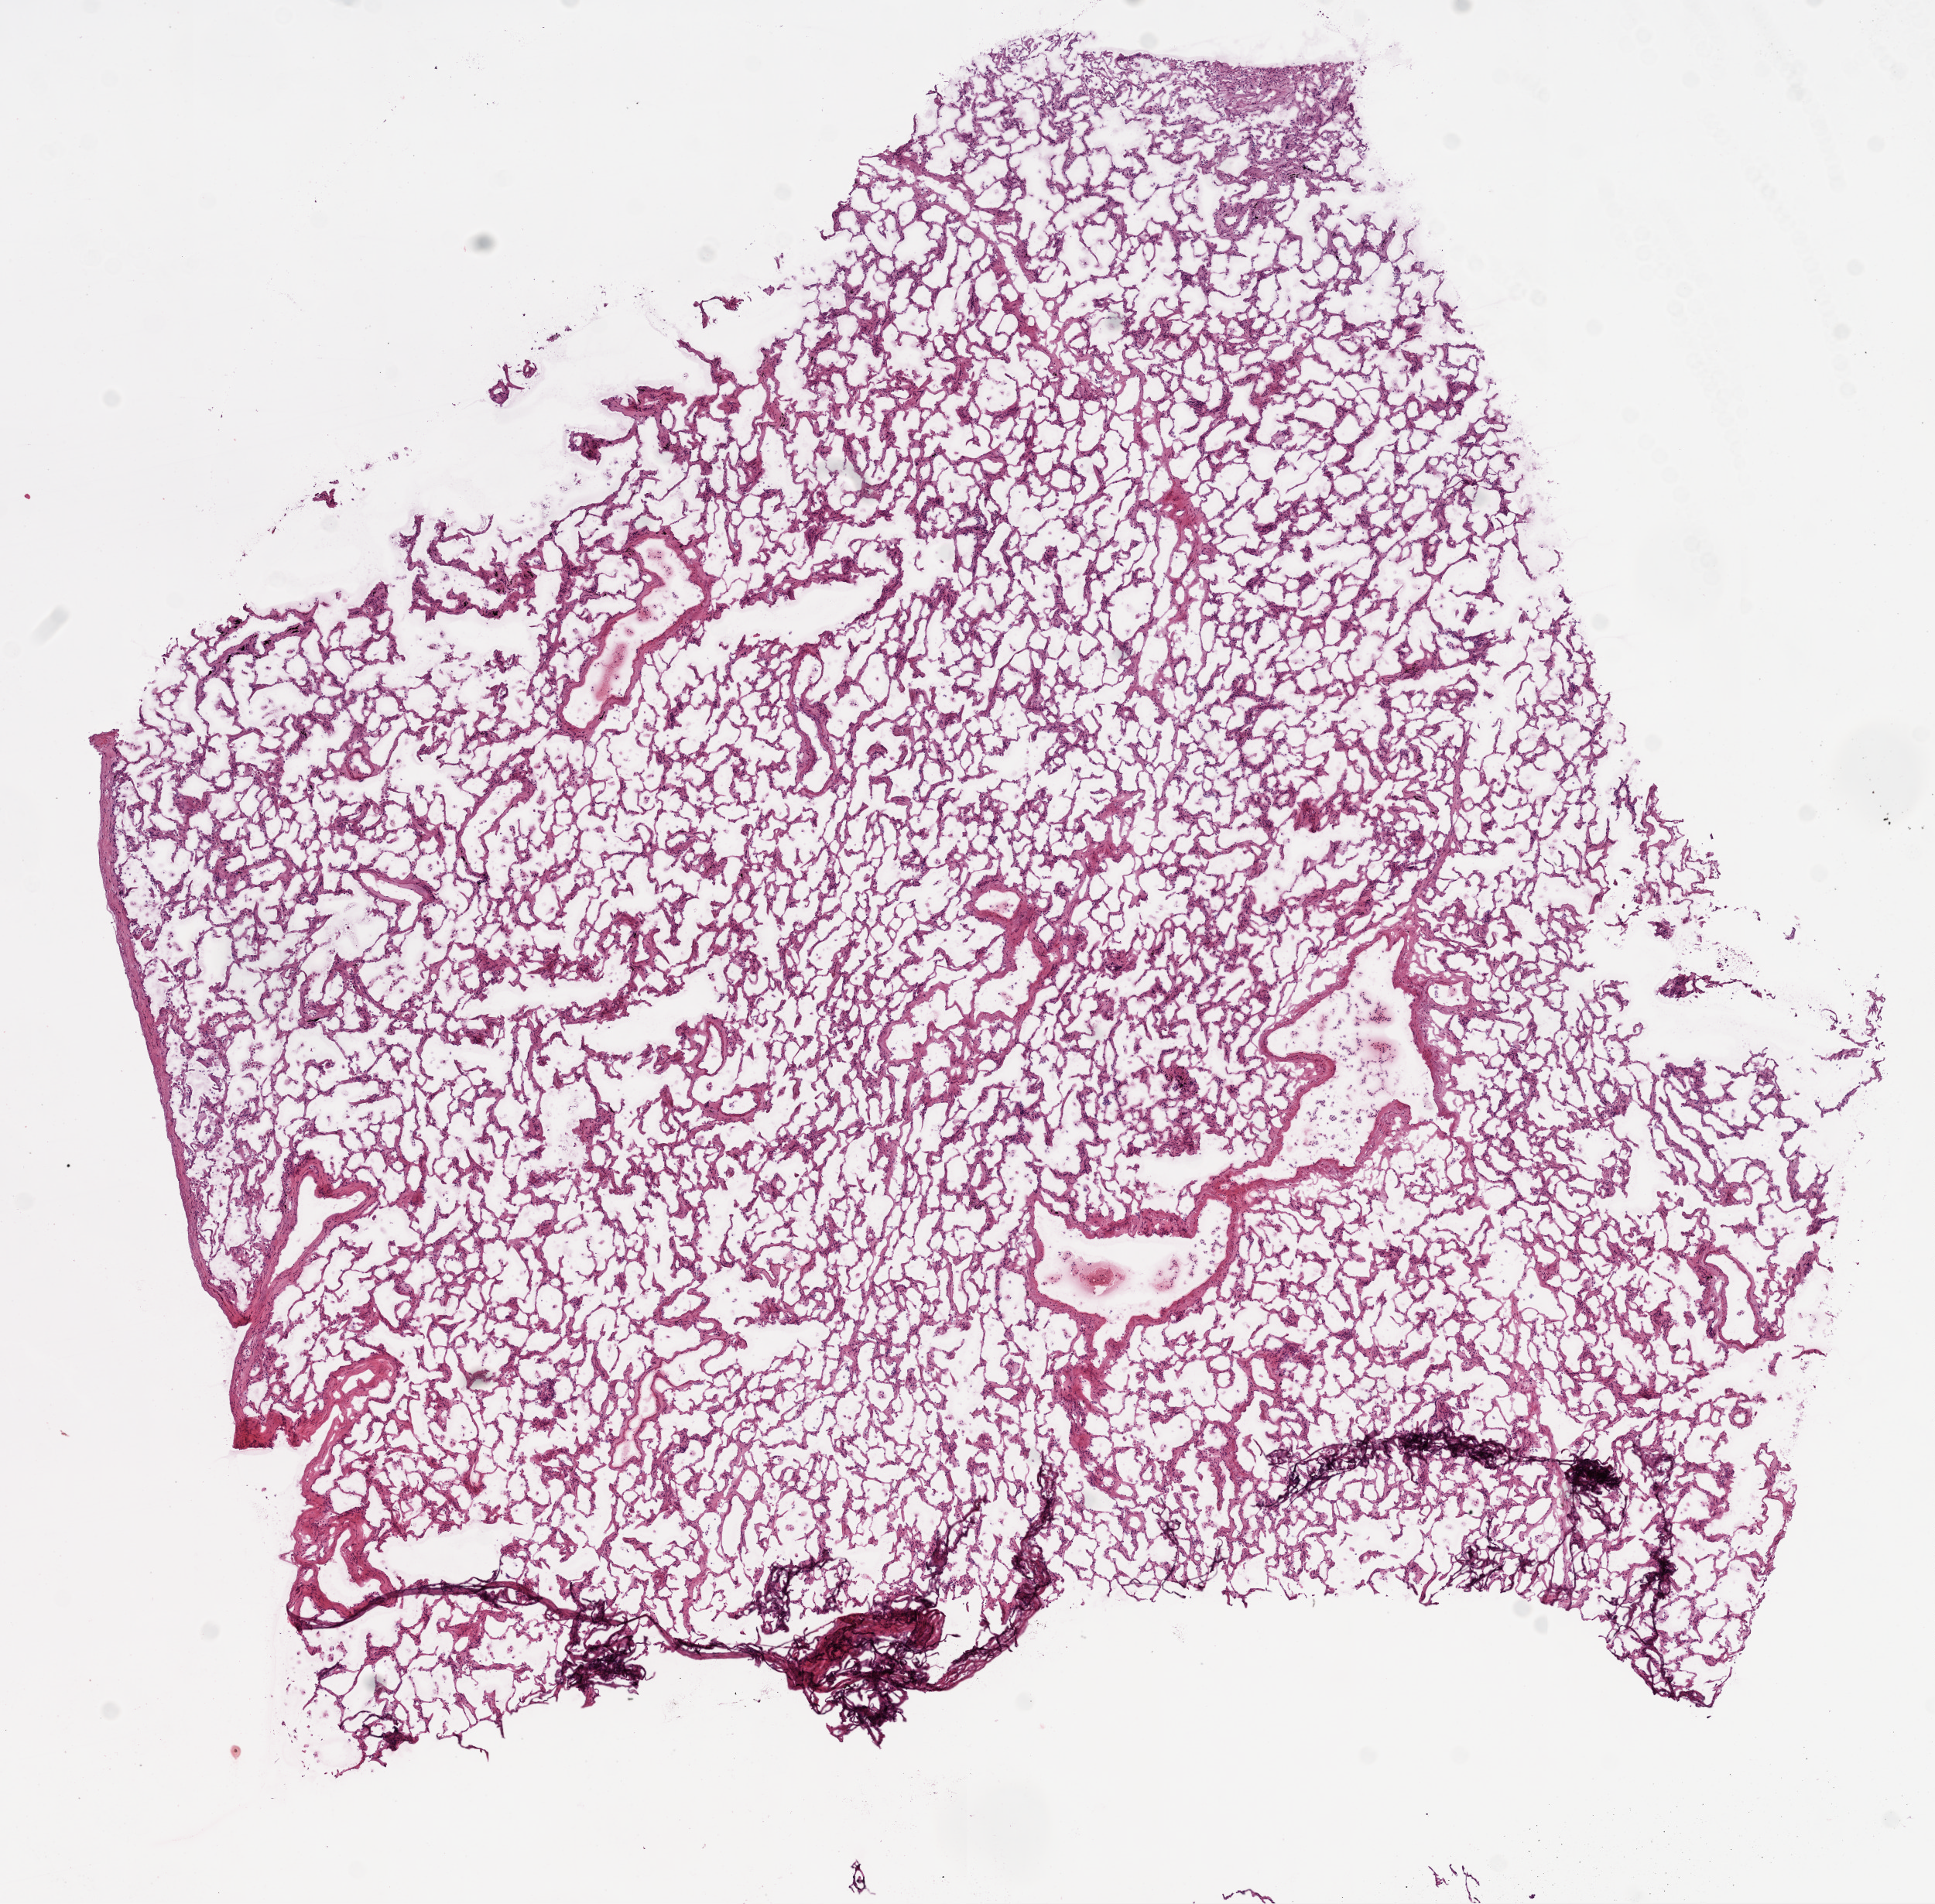
Digitized H&E-stained tissue section (whole slide) — low-resolution overview of the scanned area, about 10.0 x 9.9 mm (acquisition: 20x scan), frozen section, solid tissue normal (non-tumour tissue) sample from the lung. Female, age 73 years at initial diagnosis.
- this section: solid tissue normal sample (biorepository sample class)
- patient diagnosis: Adenocarcinoma, NOS (main bronchus)